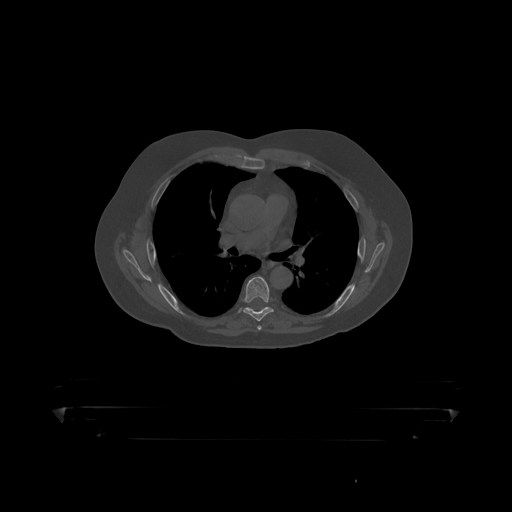
CT including the spine, one axial slice; position 299 of 390 along the scan axis; bone window (W 1800 / L 400 HU); 1.25 mm slice thickness; 512 × 512 image matrix, field of view 650 × 650 mm. Male patient, age 60 years. Case-level facts recorded for this patient, not image findings: primary cancer: prostate.
Structures marked on this image (semi-automatic segmentation, software-assisted and operator-edited):
- T6 vertebra: box from (x=243, y=277) to (x=274, y=319) px
- T7 vertebra: (x=246, y=307)–(x=268, y=310)